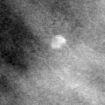
Region of interest cut from a scanned film mammogram (one marked finding); right breast; CC view.
Finding: calcifications, morphology lucent center; BI-RADS assessment category 2; benign without callback (not worked up further).